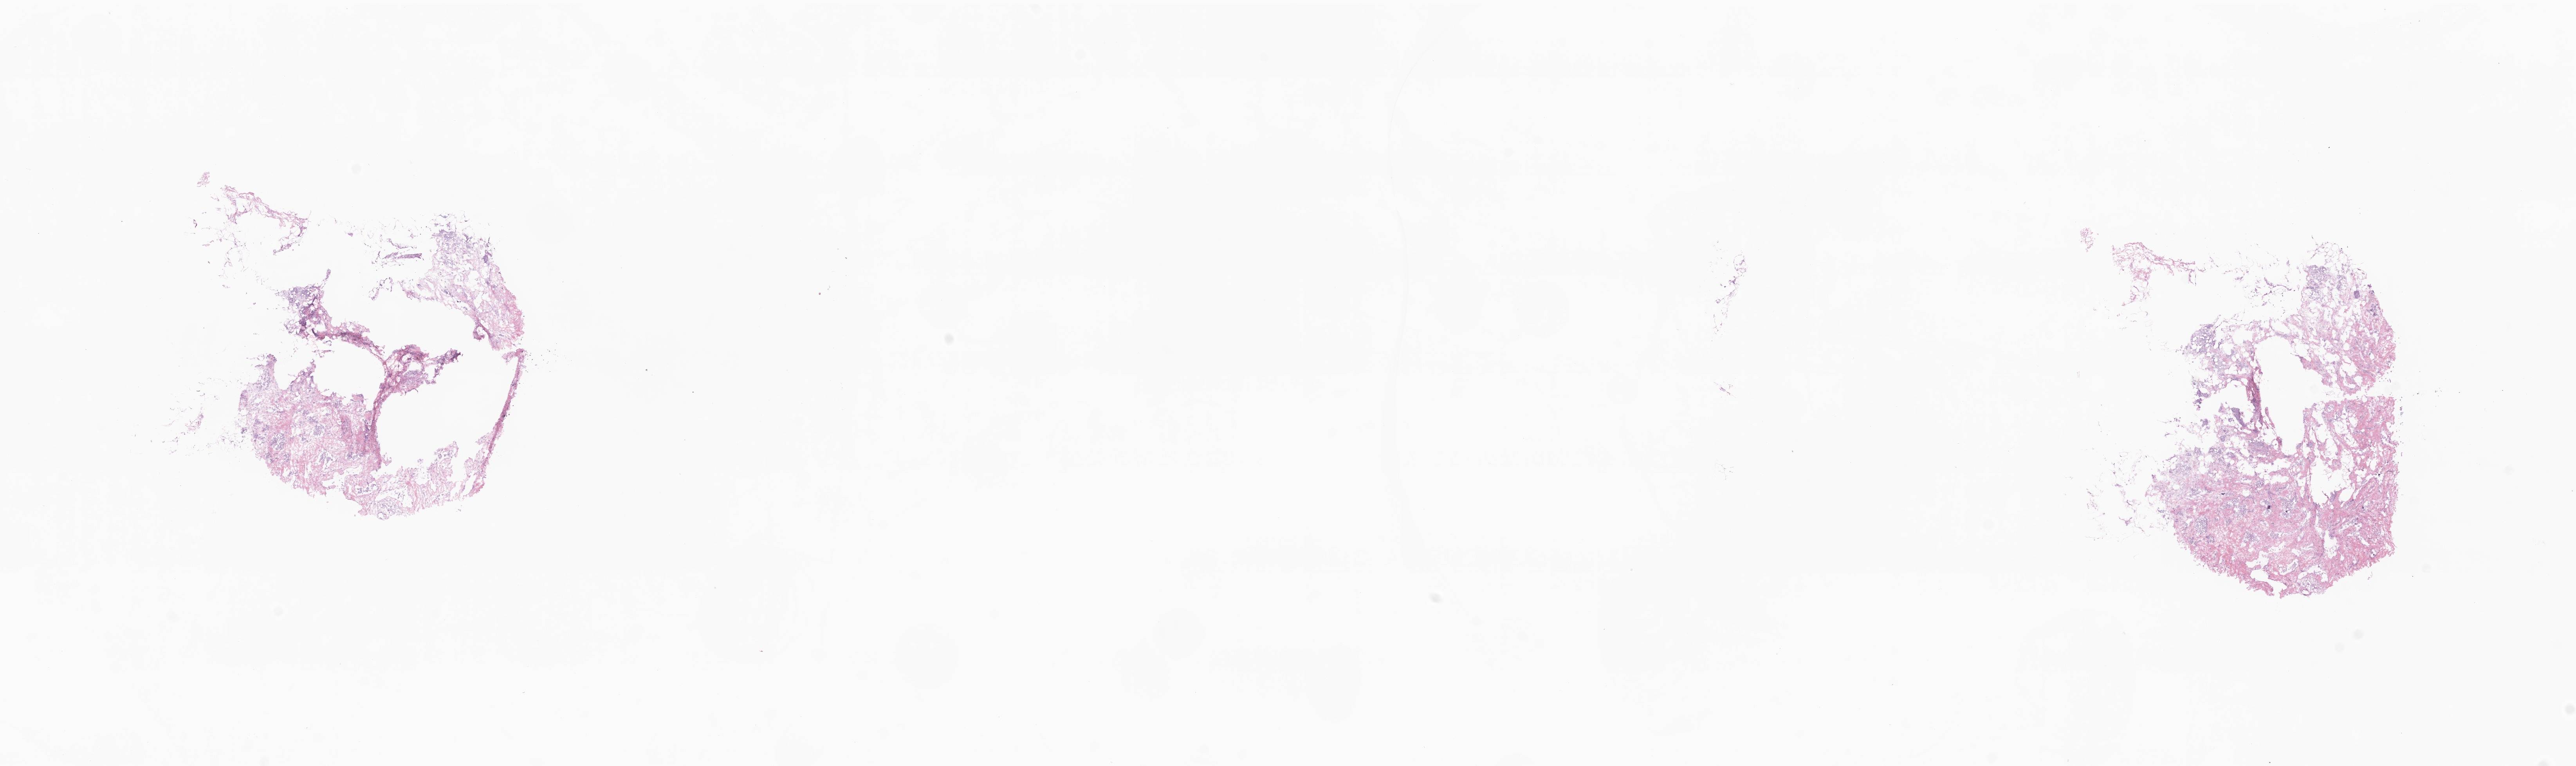
H&E whole-slide image, low-resolution overview of the scanned area, about 27.7 x 8.2 mm, frozen section (tissue freezing medium), primary tumor, site: breast (left). Patient: female, age at initial diagnosis 82 years. Composition of this section per pathologist review: tumor cells 95%, tumor nuclei 80%, stromal cells 0%, necrosis 0%, normal cells 5%. Inflammatory infiltration, as recorded: lymphocyte infiltration 0%, monocyte infiltration 0%, neutrophil infiltration 0%.
• histologic diagnosis: Infiltrating duct carcinoma, NOS
• section: bottom of the tissue portion